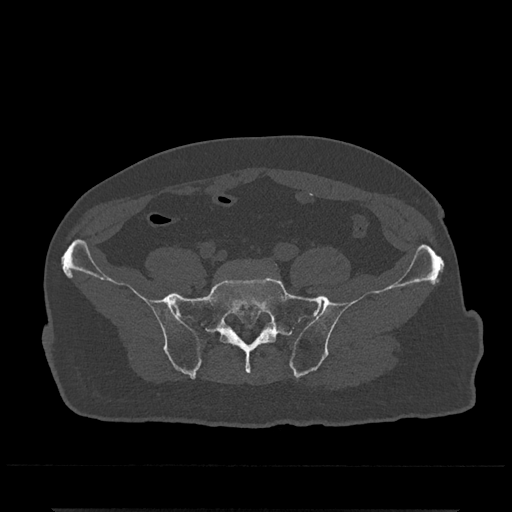
CT including the spine, one axial slice. Bone window (W 1800 / L 400 HU). 0.5 mm slice thickness. 512 × 512 image matrix, field of view 393 × 393 mm. Patient: male, 67 years. Case-level facts recorded for this patient, not image findings: primary cancer: prostate.
Outlined on this slice (semi-automatically segmented with operator editing):
- L5 vertebra: box from (x=273, y=262) to (x=277, y=266) px